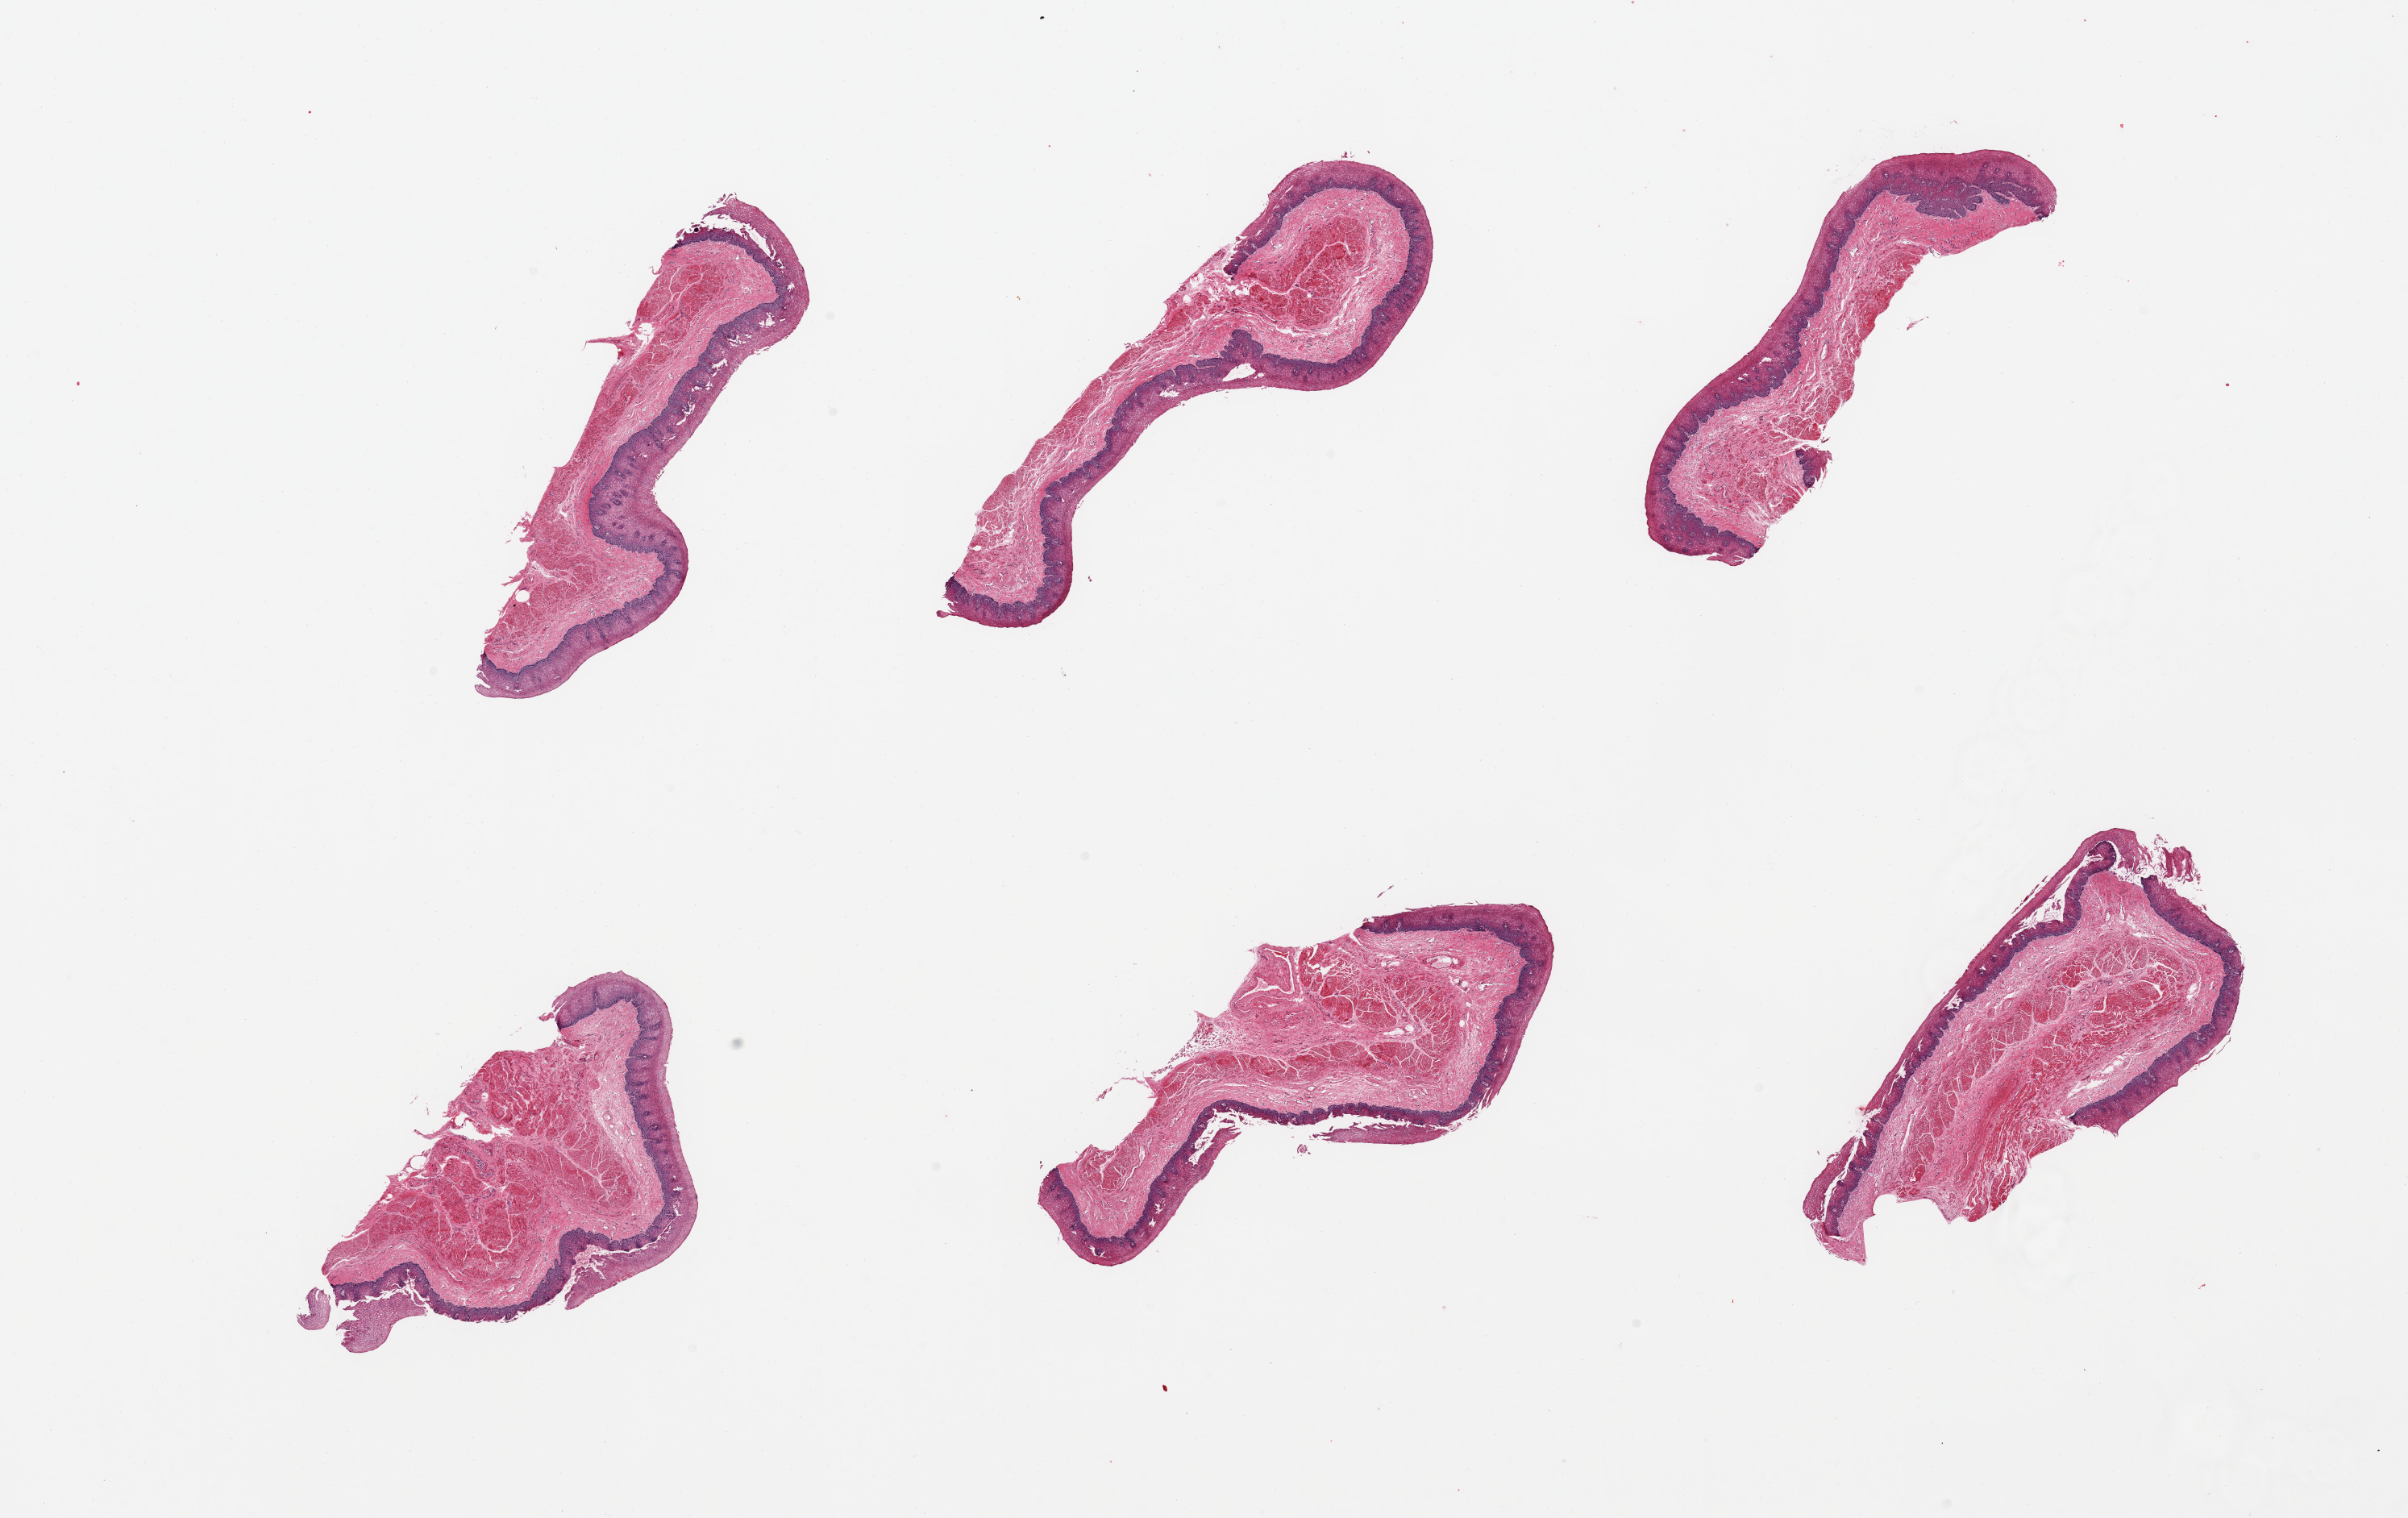
Whole-slide image, haematoxylin and eosin stain, brightfield, a low-resolution overview of the entire scanned area, about 23.6 x 14.9 mm, PAXgene-fixed, paraffin-embedded tissue, target tissue: esophageal mucous membrane, donor tissue sample. Female donor.
• review note (as recorded): 6 pieces; epithelium 'fractured'